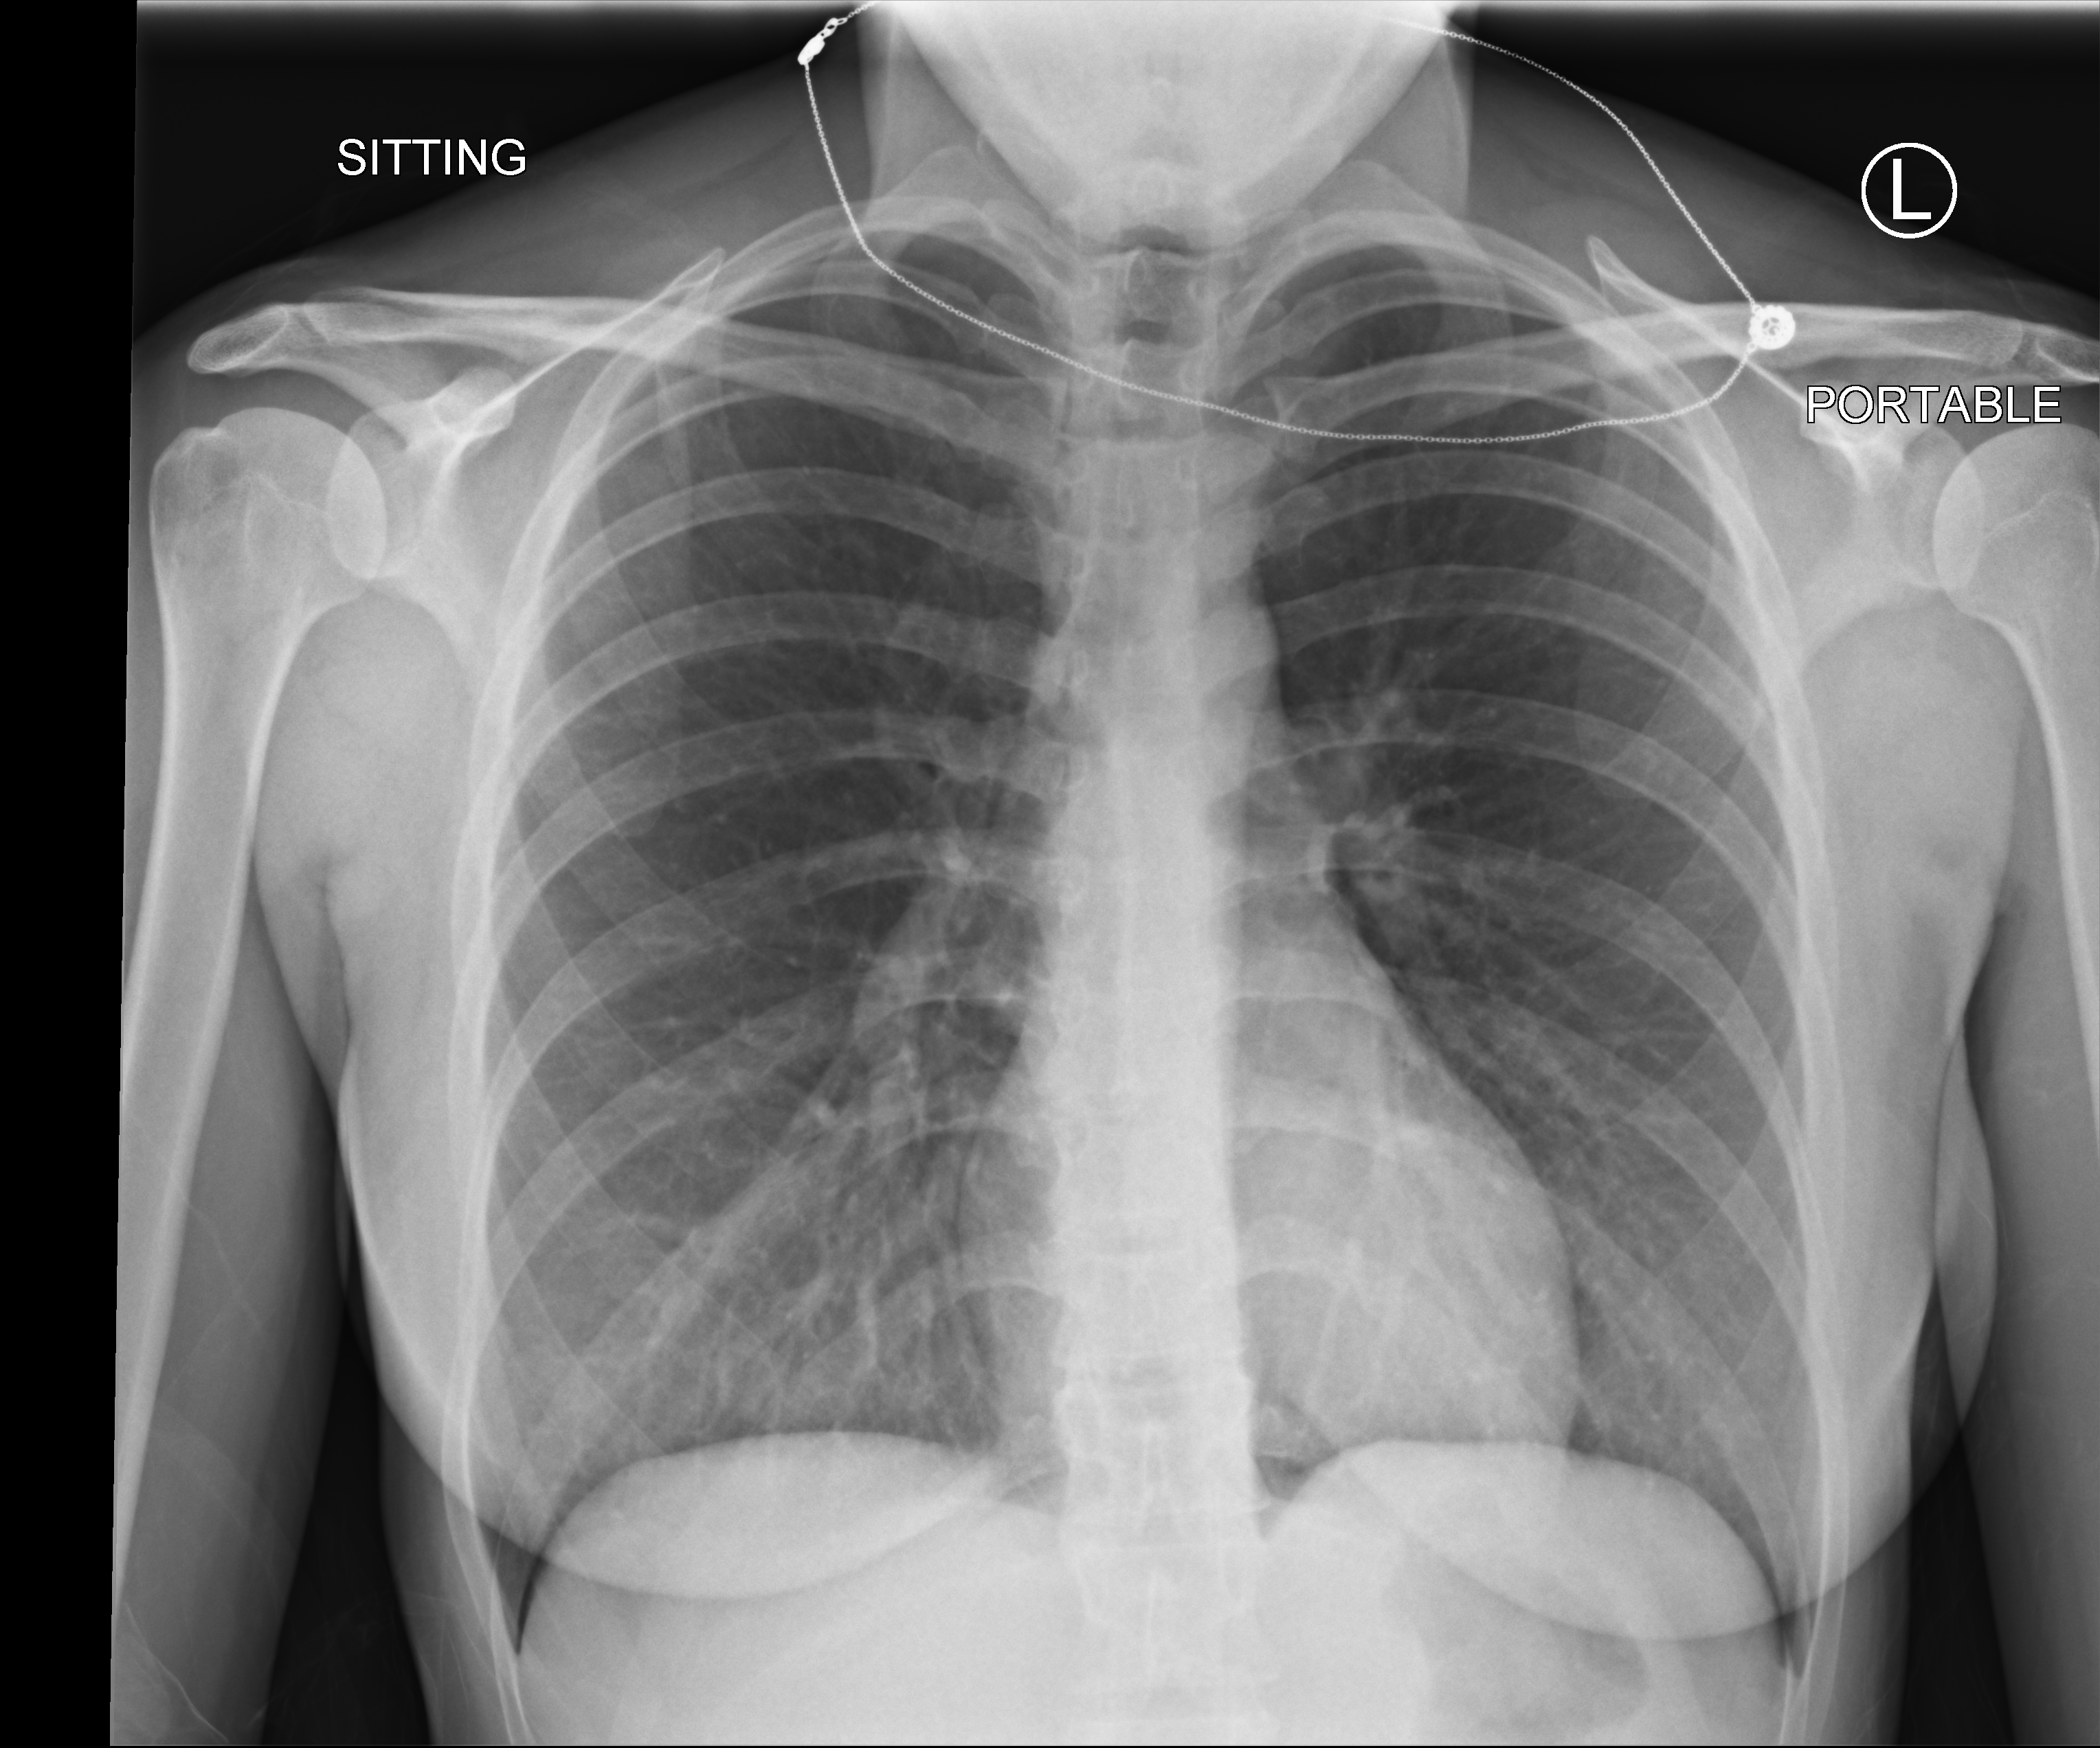
Chest X-ray (portable); anteroposterior (AP) projection. Patient hospitalised with COVID-19; female, aged 18–59 years.
From the hospital-stay record, not from the radiograph (when in the stay this image was taken is not recorded):
- admitted to intensive care during this hospital stay: no